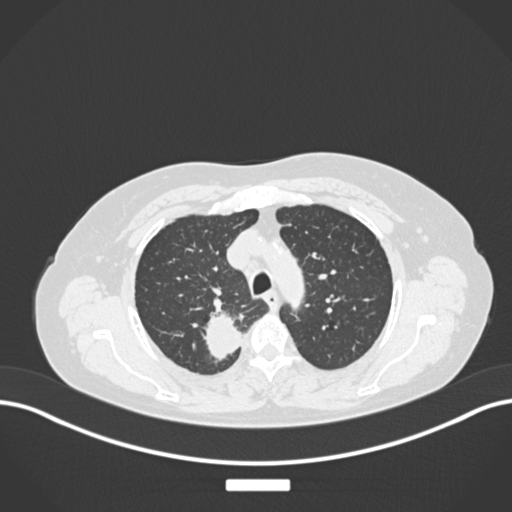
Chest CT, one axial slice. Reconstruction kernel B30f. Lung window (W 1500 / L -600 HU). 512 × 512 image matrix, field of view 400 × 400 mm. Patient: female, 62 years. Case-level facts recorded for this patient, not image findings: clinical TNM (as recorded): T1c N1 M0.
Annotated regions visible in this slice (bounding box drawn by a radiologist):
- lung tumour (recorded histology: squamous cell carcinoma): box from (x=202, y=314) to (x=242, y=364) px